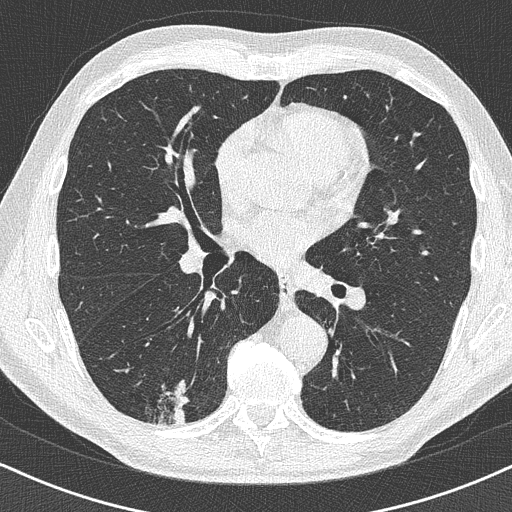
Chest CT (low-dose screening protocol), one axial image, first (baseline) screen, lung window (W 1500 / L -600 HU), slice 214 of 438 in the series. Male, age 63 years at enrolment. Former smoker at enrolment.
Lesion marked by an expert reader, bounding box <134,368,206,430> (left, top, right, bottom; pixels). Reader record for this screening exam (exam-level; its link to the box is not recorded): non-calcified nodule or mass ≥4 mm, right lower lobe, 16 × 13 mm, poorly defined margins. Participant outcome: lung cancer diagnosed 74 days after this screen — adenocarcinoma, NOS, right lower lobe, moderately differentiated (G2), stage IA (AJCC 6th edition), 20 mm at pathology.